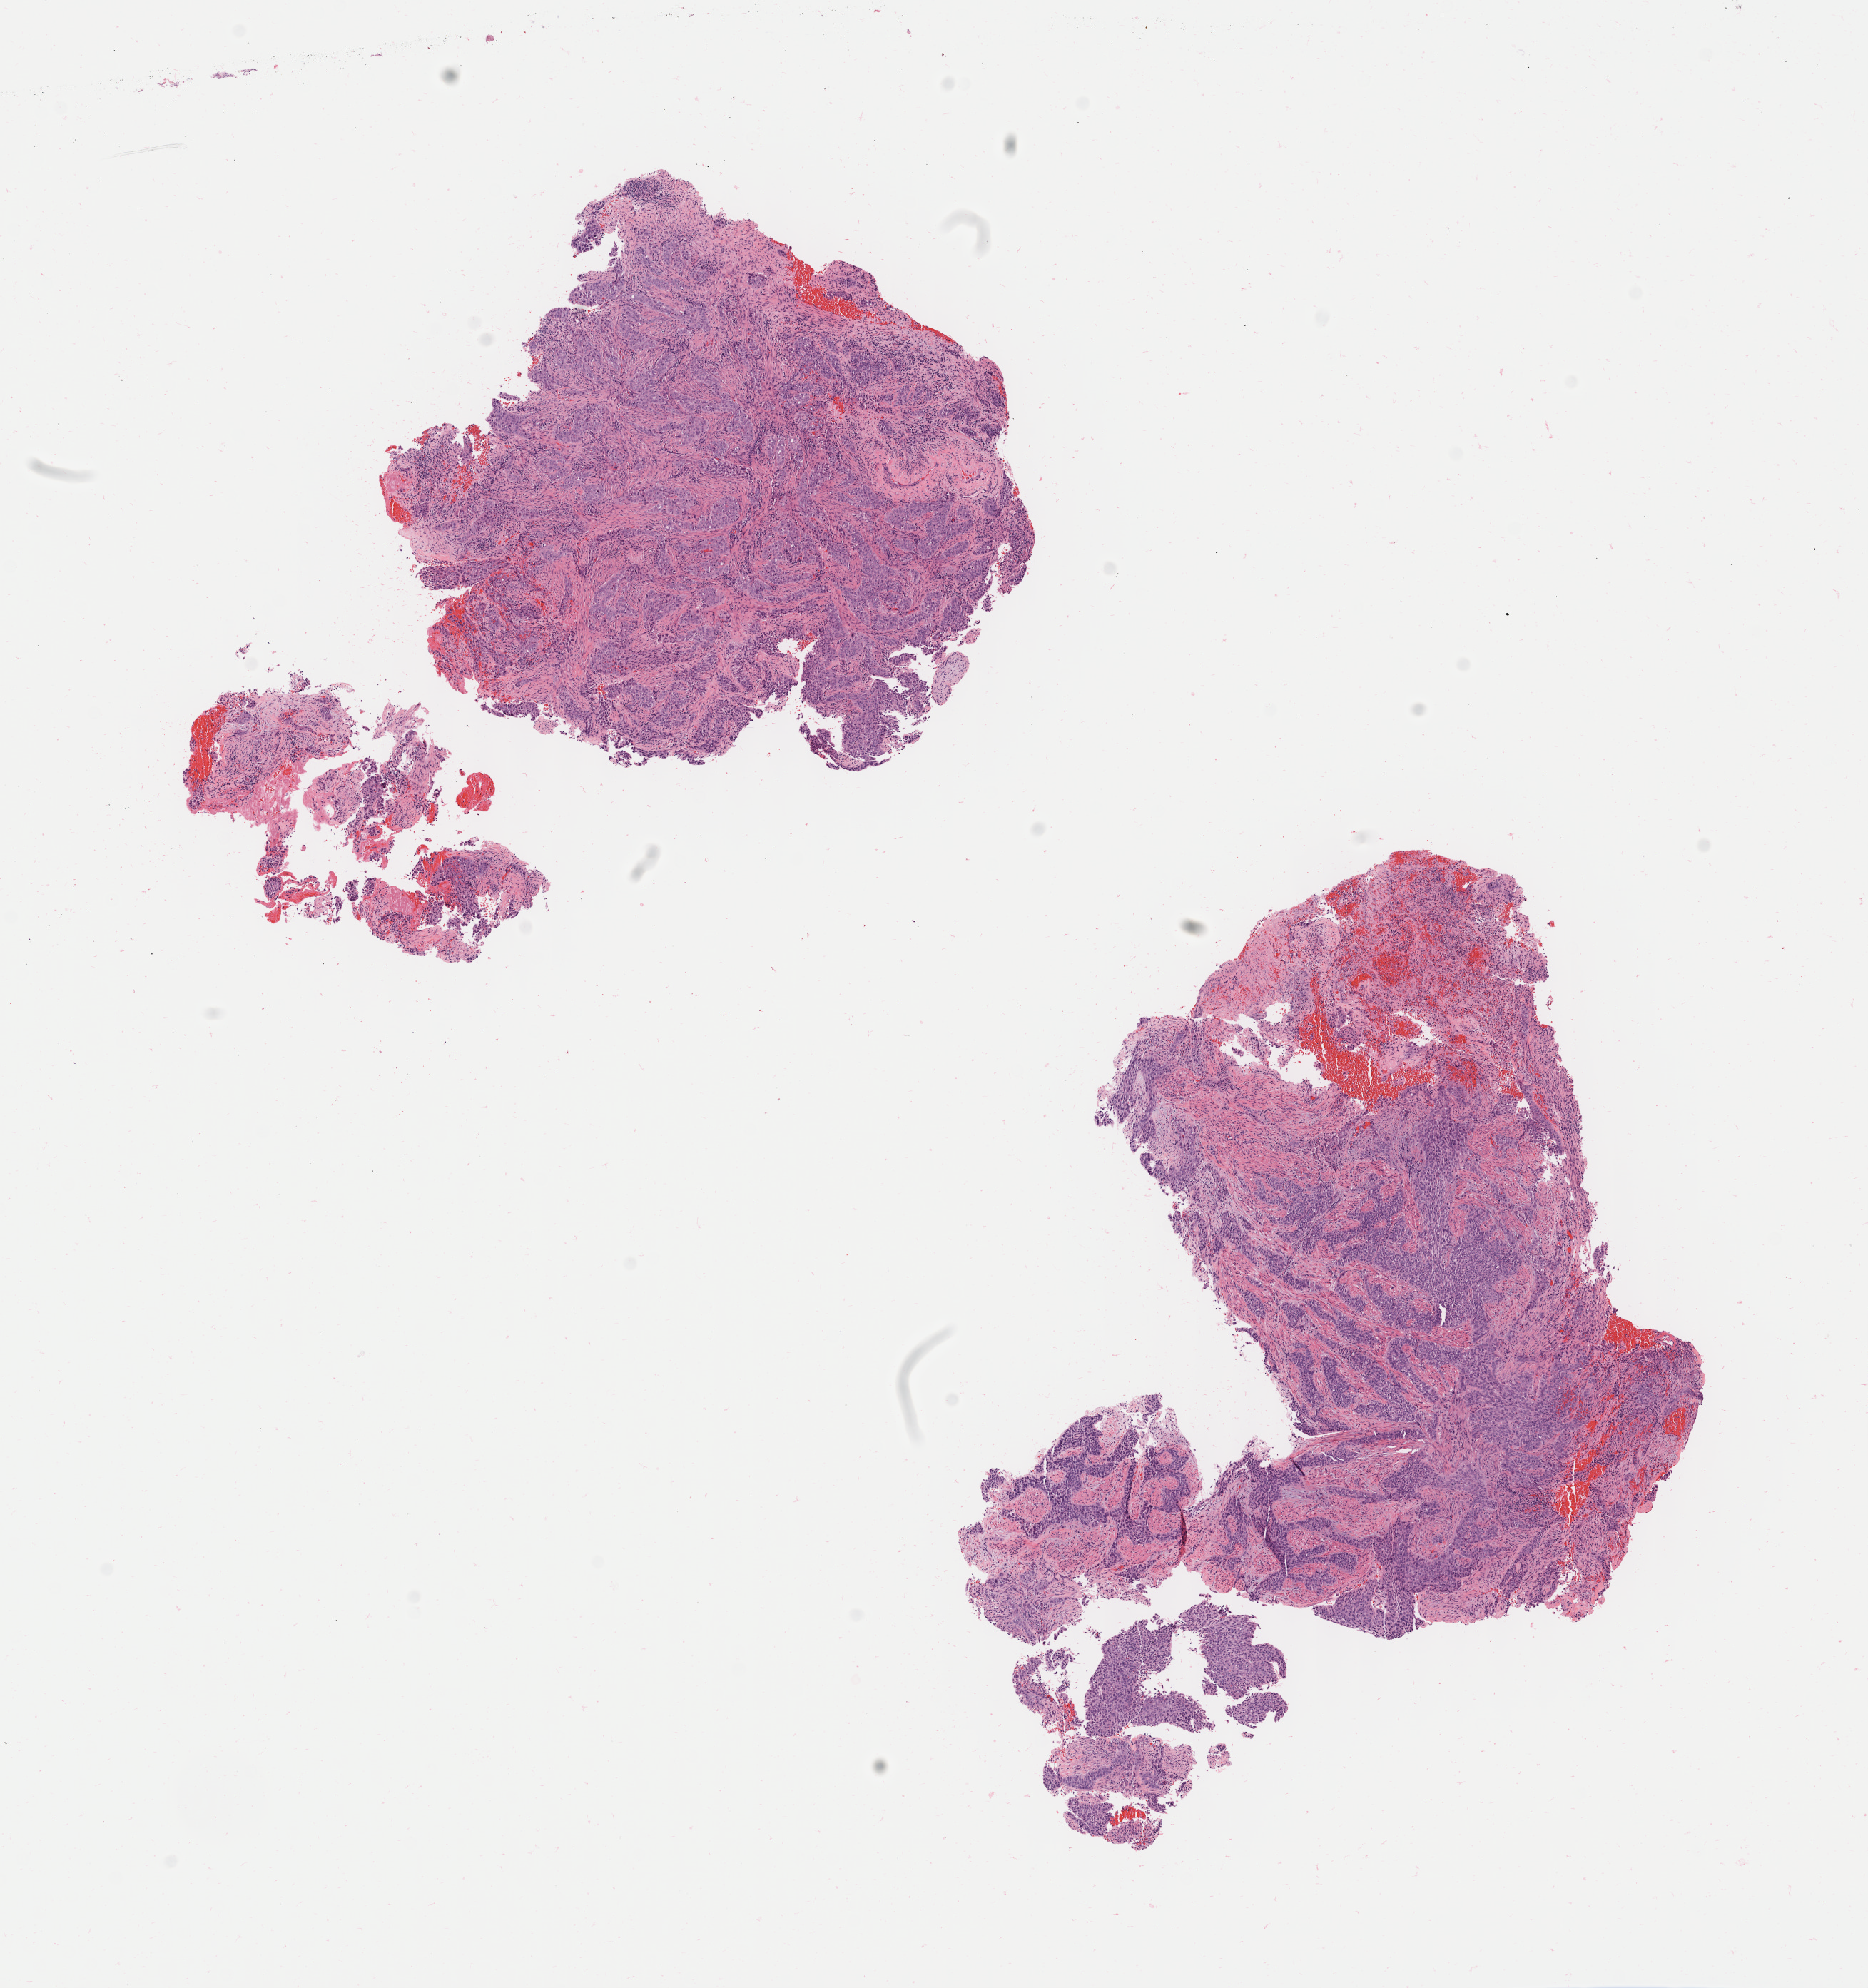
H&E whole-slide image, whole scanned area (about 10.4 x 11.1 mm) shown as a low-resolution overview. Specimen: tumor tissue. Site: cervix. Patient: female, 66 years old.
- diagnosis: Squamous cell carcinoma, large cell, nonkeratinizing, NOS